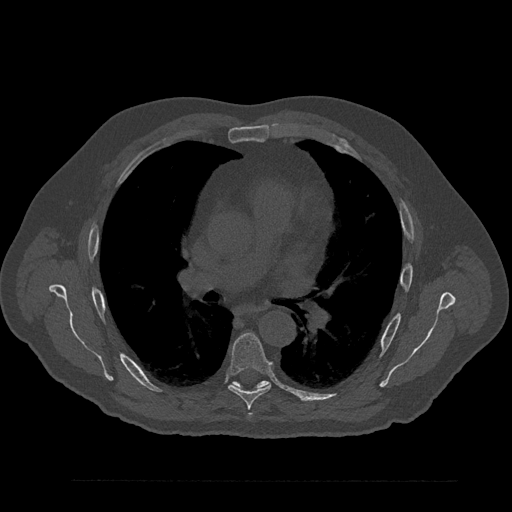
CT including the spine, one axial slice; position 545 of 797 along the scan axis; 120 kVp; bone window (W 1800 / L 400 HU); 0.5 mm slice thickness; 512 × 512 image matrix. Patient: male, 61 years. From the clinical record (not read from this slice): primary cancer: prostate.
Structures marked on this image (semi-automatically segmented with operator editing):
- T6 vertebra: box from (x=228, y=333) to (x=272, y=418) px
- T7 vertebra: (x=236, y=380)–(x=269, y=388)